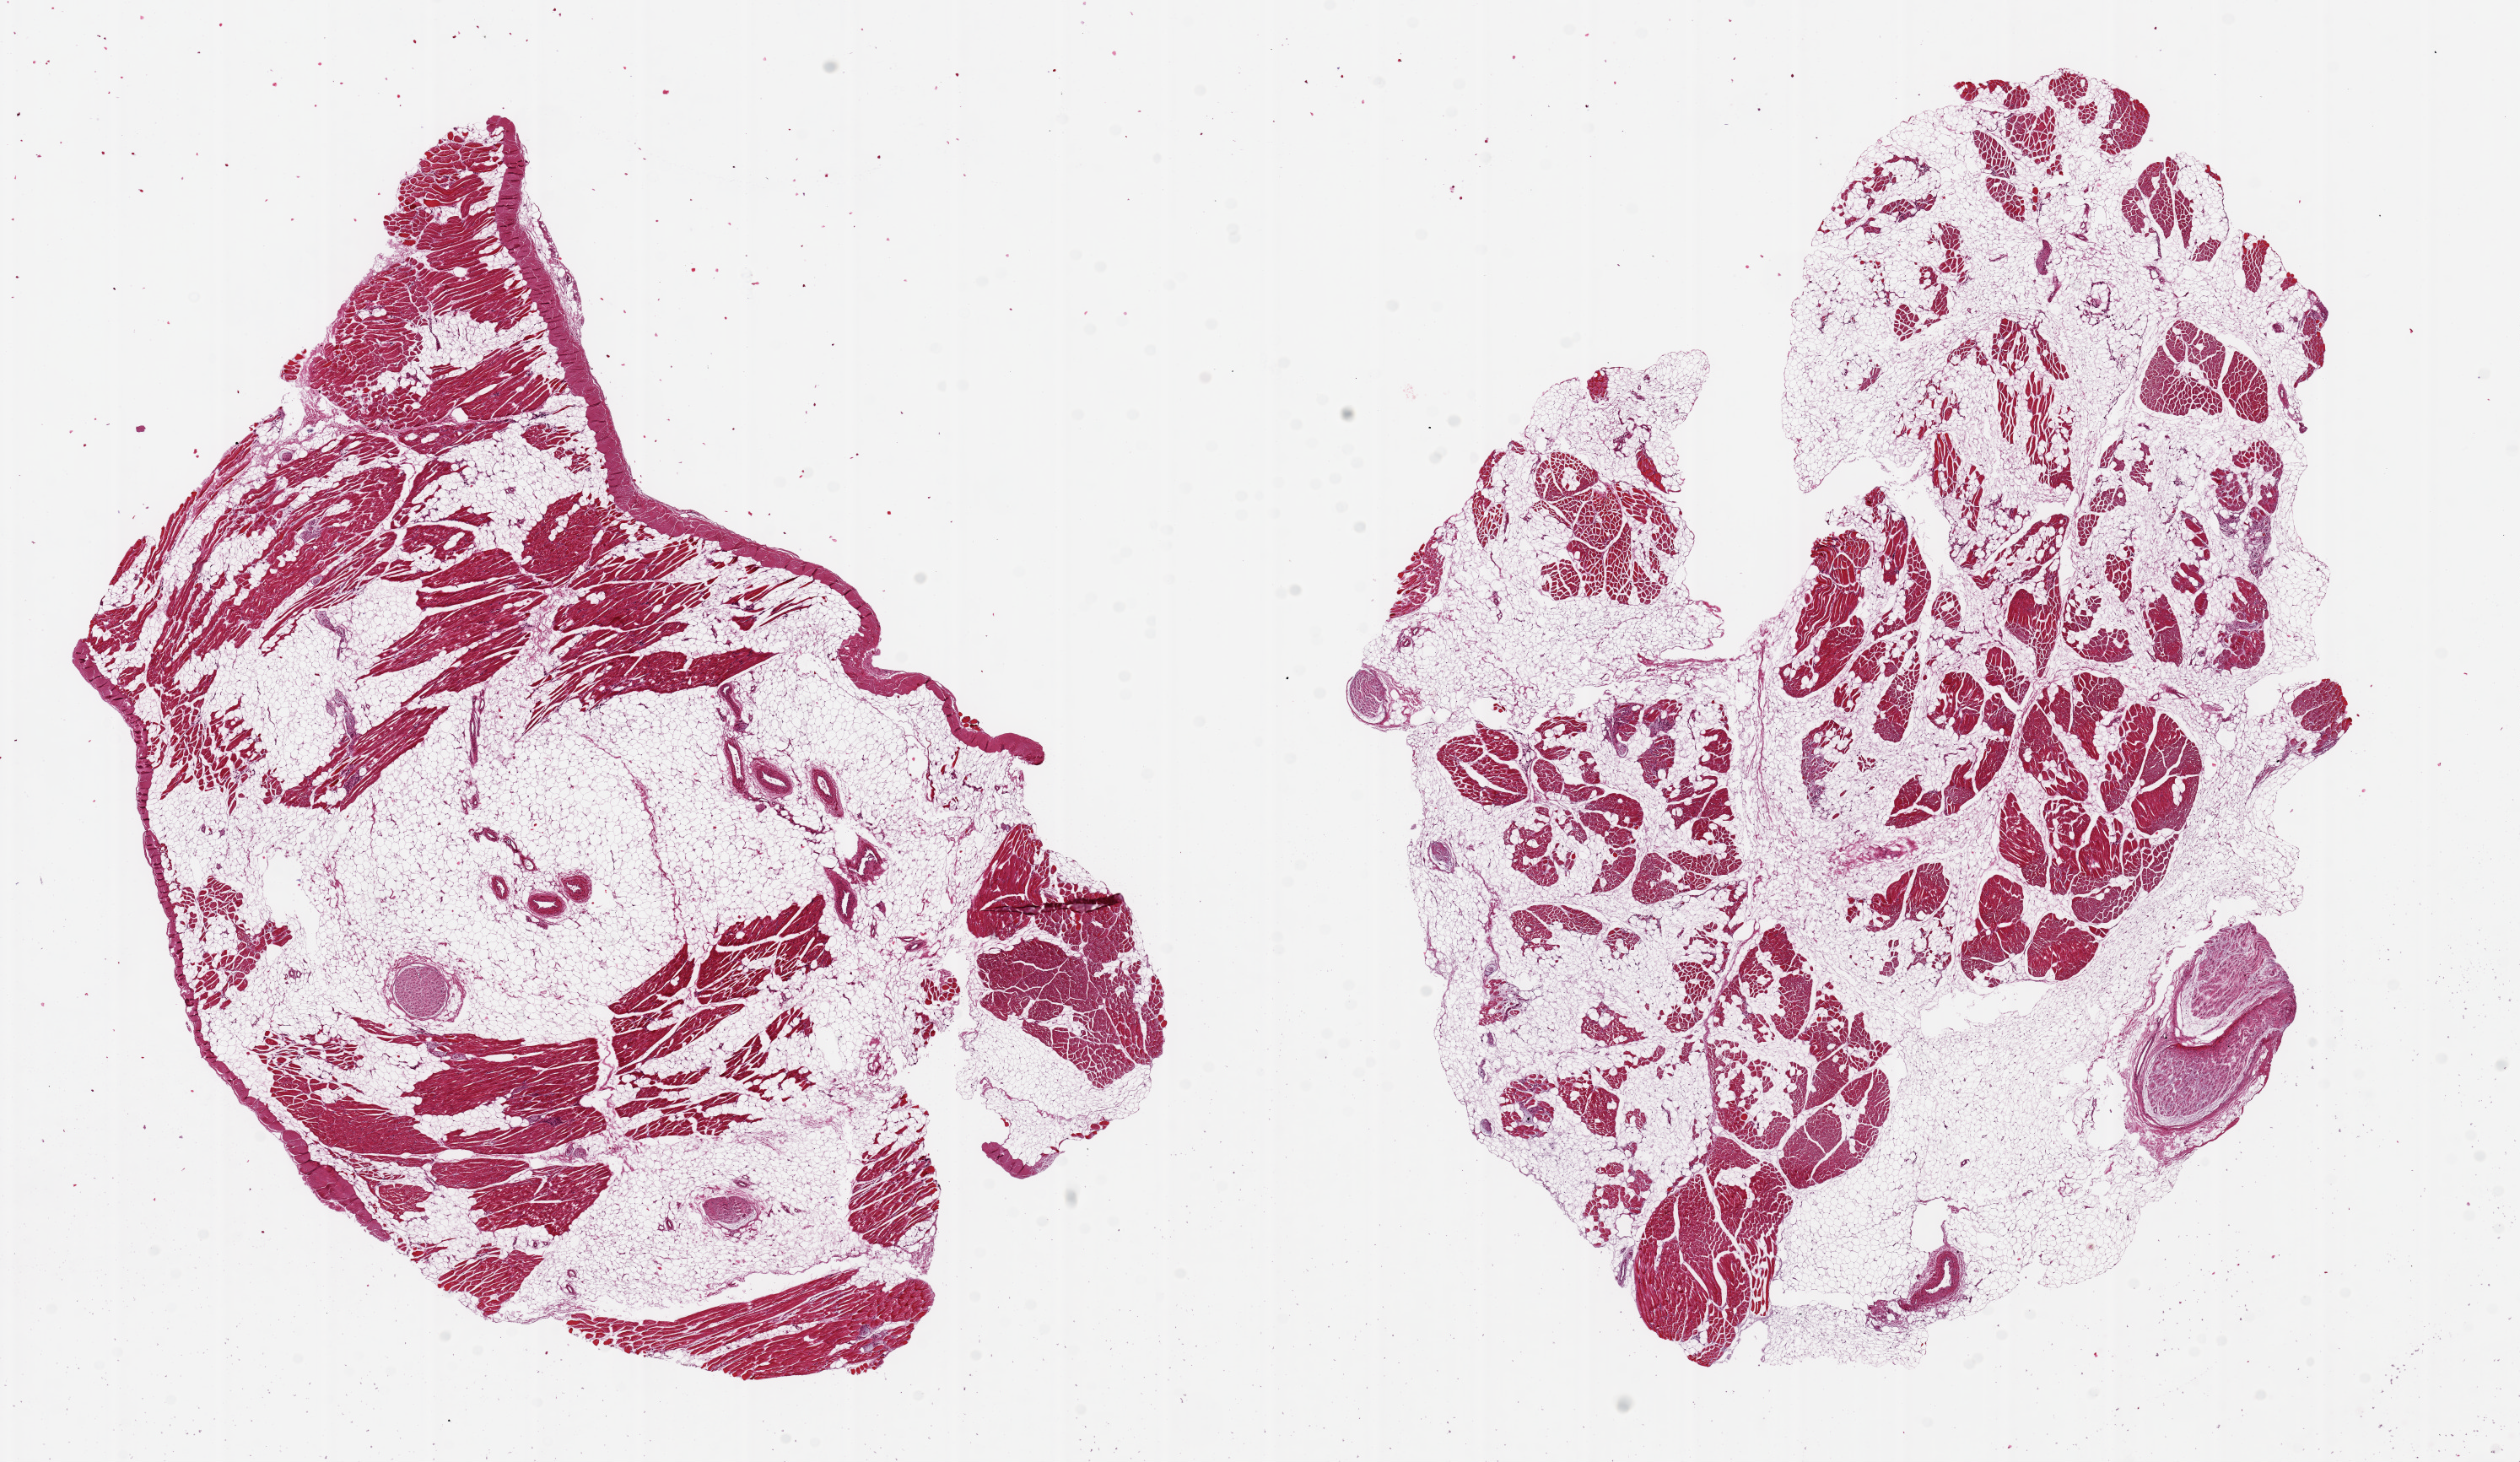
Hematoxylin and eosin (H&E) whole-slide image, brightfield, whole scanned area (about 23.6 x 13.7 mm) shown as a low-resolution overview. Donor: female.
- specimen: PAXgene-fixed, paraffin-embedded tissue; section of skeletal muscle (target tissue); donor tissue sample